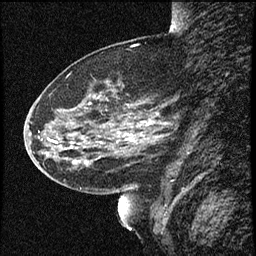
Breast MRI (dynamic contrast-enhanced), one sagittal slice; position 22 of 60 along the scan axis; dynamic contrast-enhanced study with each time point stored as its own series, time point 2 of 4 at this slice position (early post-contrast, ordered by acquisition time); 1.5 T; TE 4.2 ms, TR 16.7 ms; 2 mm slice thickness; 256 × 256 image matrix. Patient: female, 52 years. Case-level facts recorded for this patient, not image findings: setting: breast cancer imaged before/during neoadjuvant chemotherapy; receptor status: HER2-positive.
Annotated regions visible in this slice (semi-automatically segmented with operator editing):
- analysis volume of interest (the breast-tissue region the enhancement analysis was run in; not a lesion): box from (x=37, y=79) to (x=165, y=181) px
- tumour enhancement mask (voxels above the 100 % enhancement threshold inside the analysis volume of interest): (x=85, y=137)–(x=134, y=164)